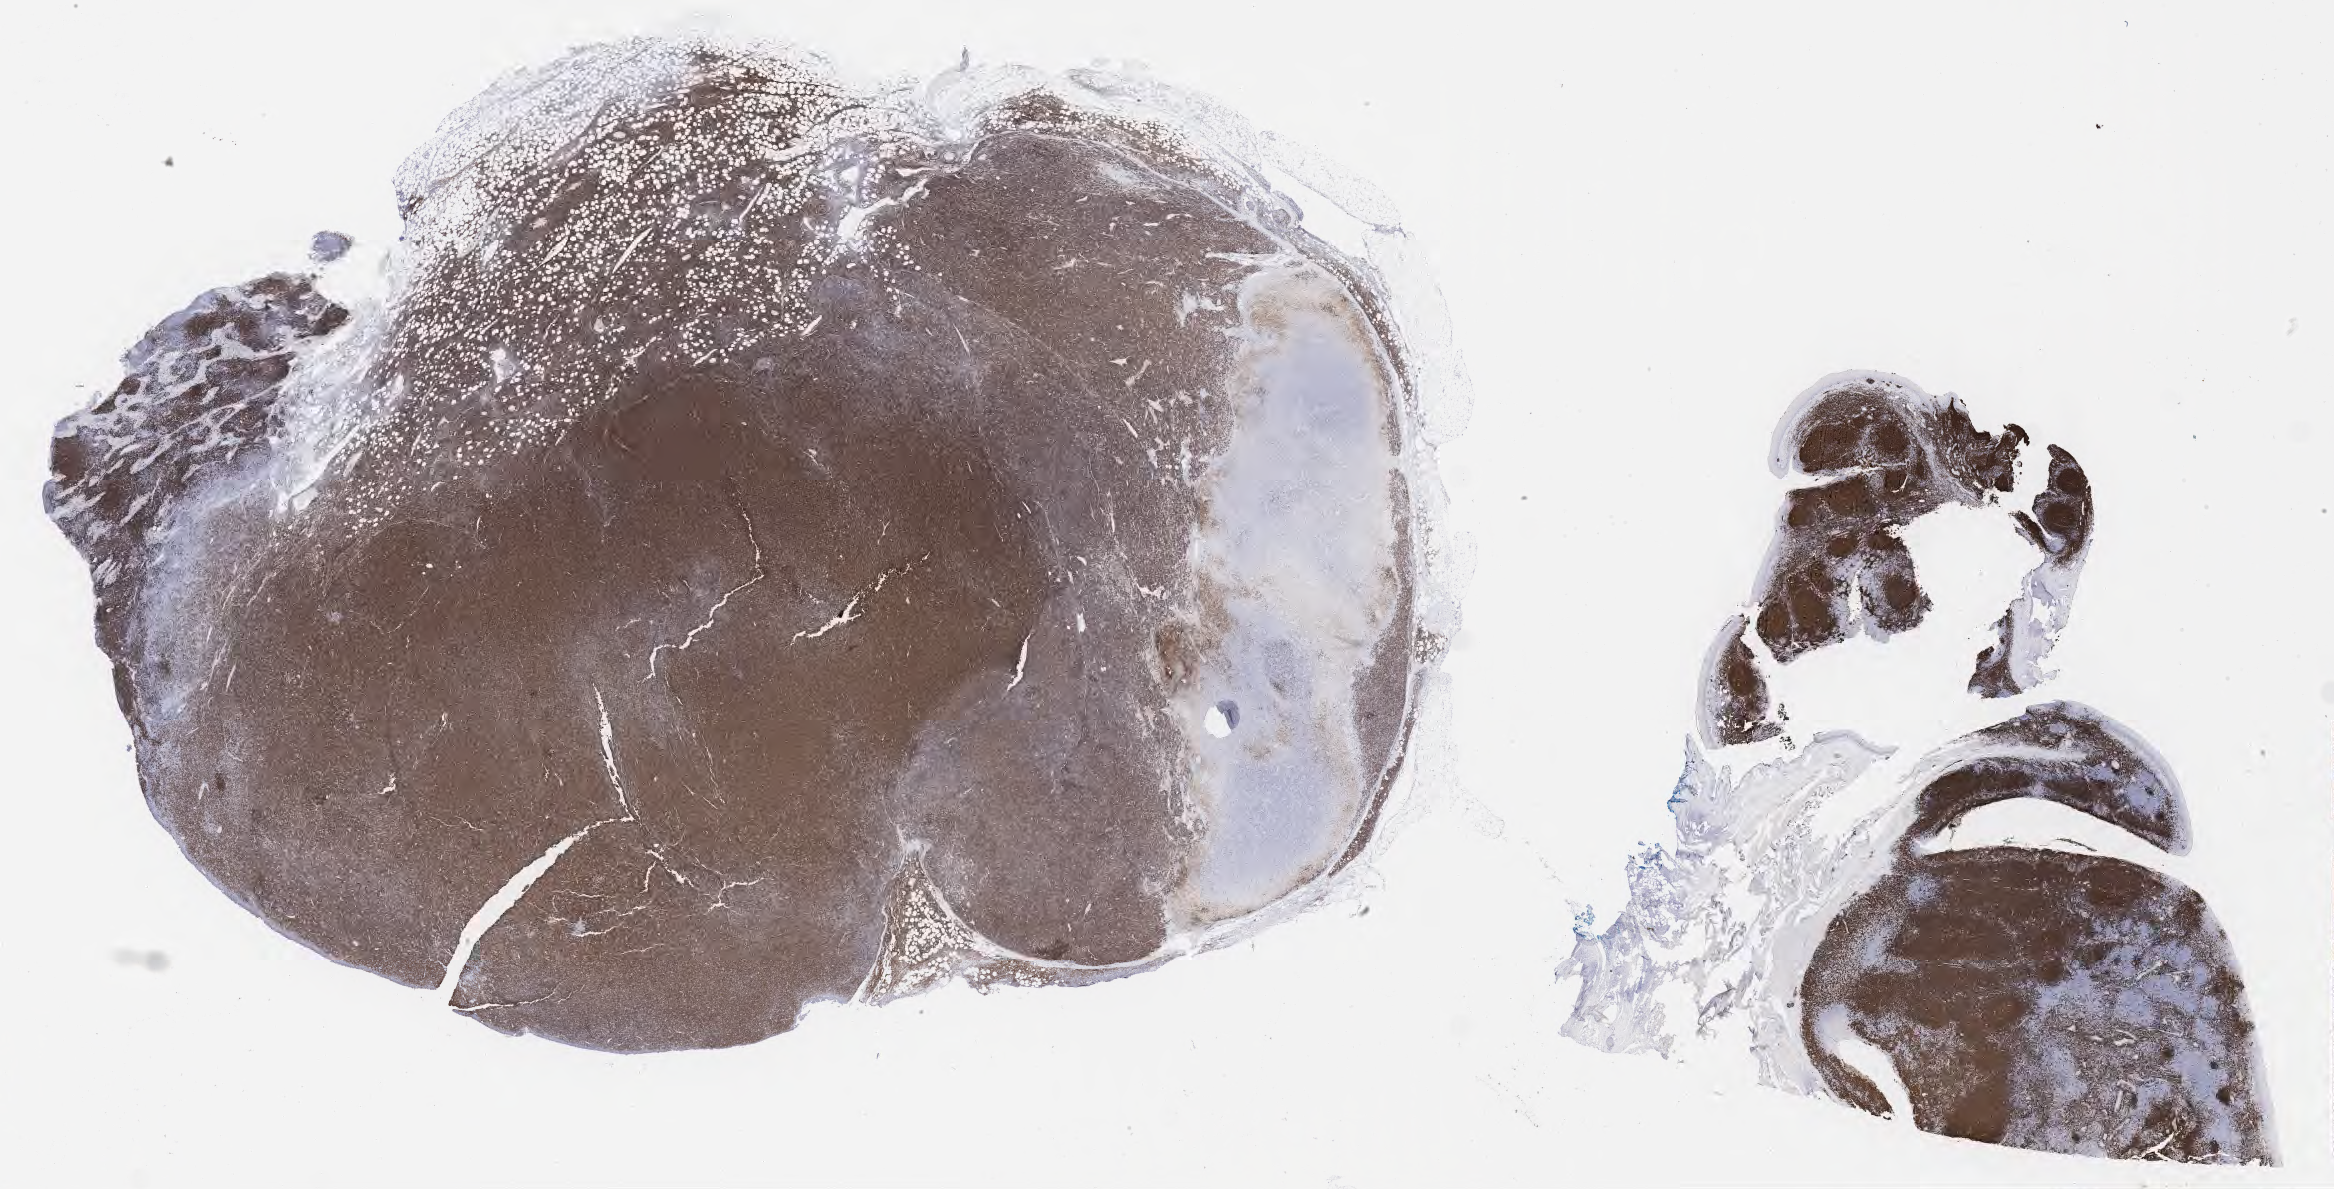
Immunohistochemistry (IHC) whole-slide image stained for CD20 — low-resolution overview of the scanned area, about 37.7 x 19.2 mm, tumor tissue. Male patient, age 57 years.
Histologic diagnosis: Burkitt lymphoma, NOS.